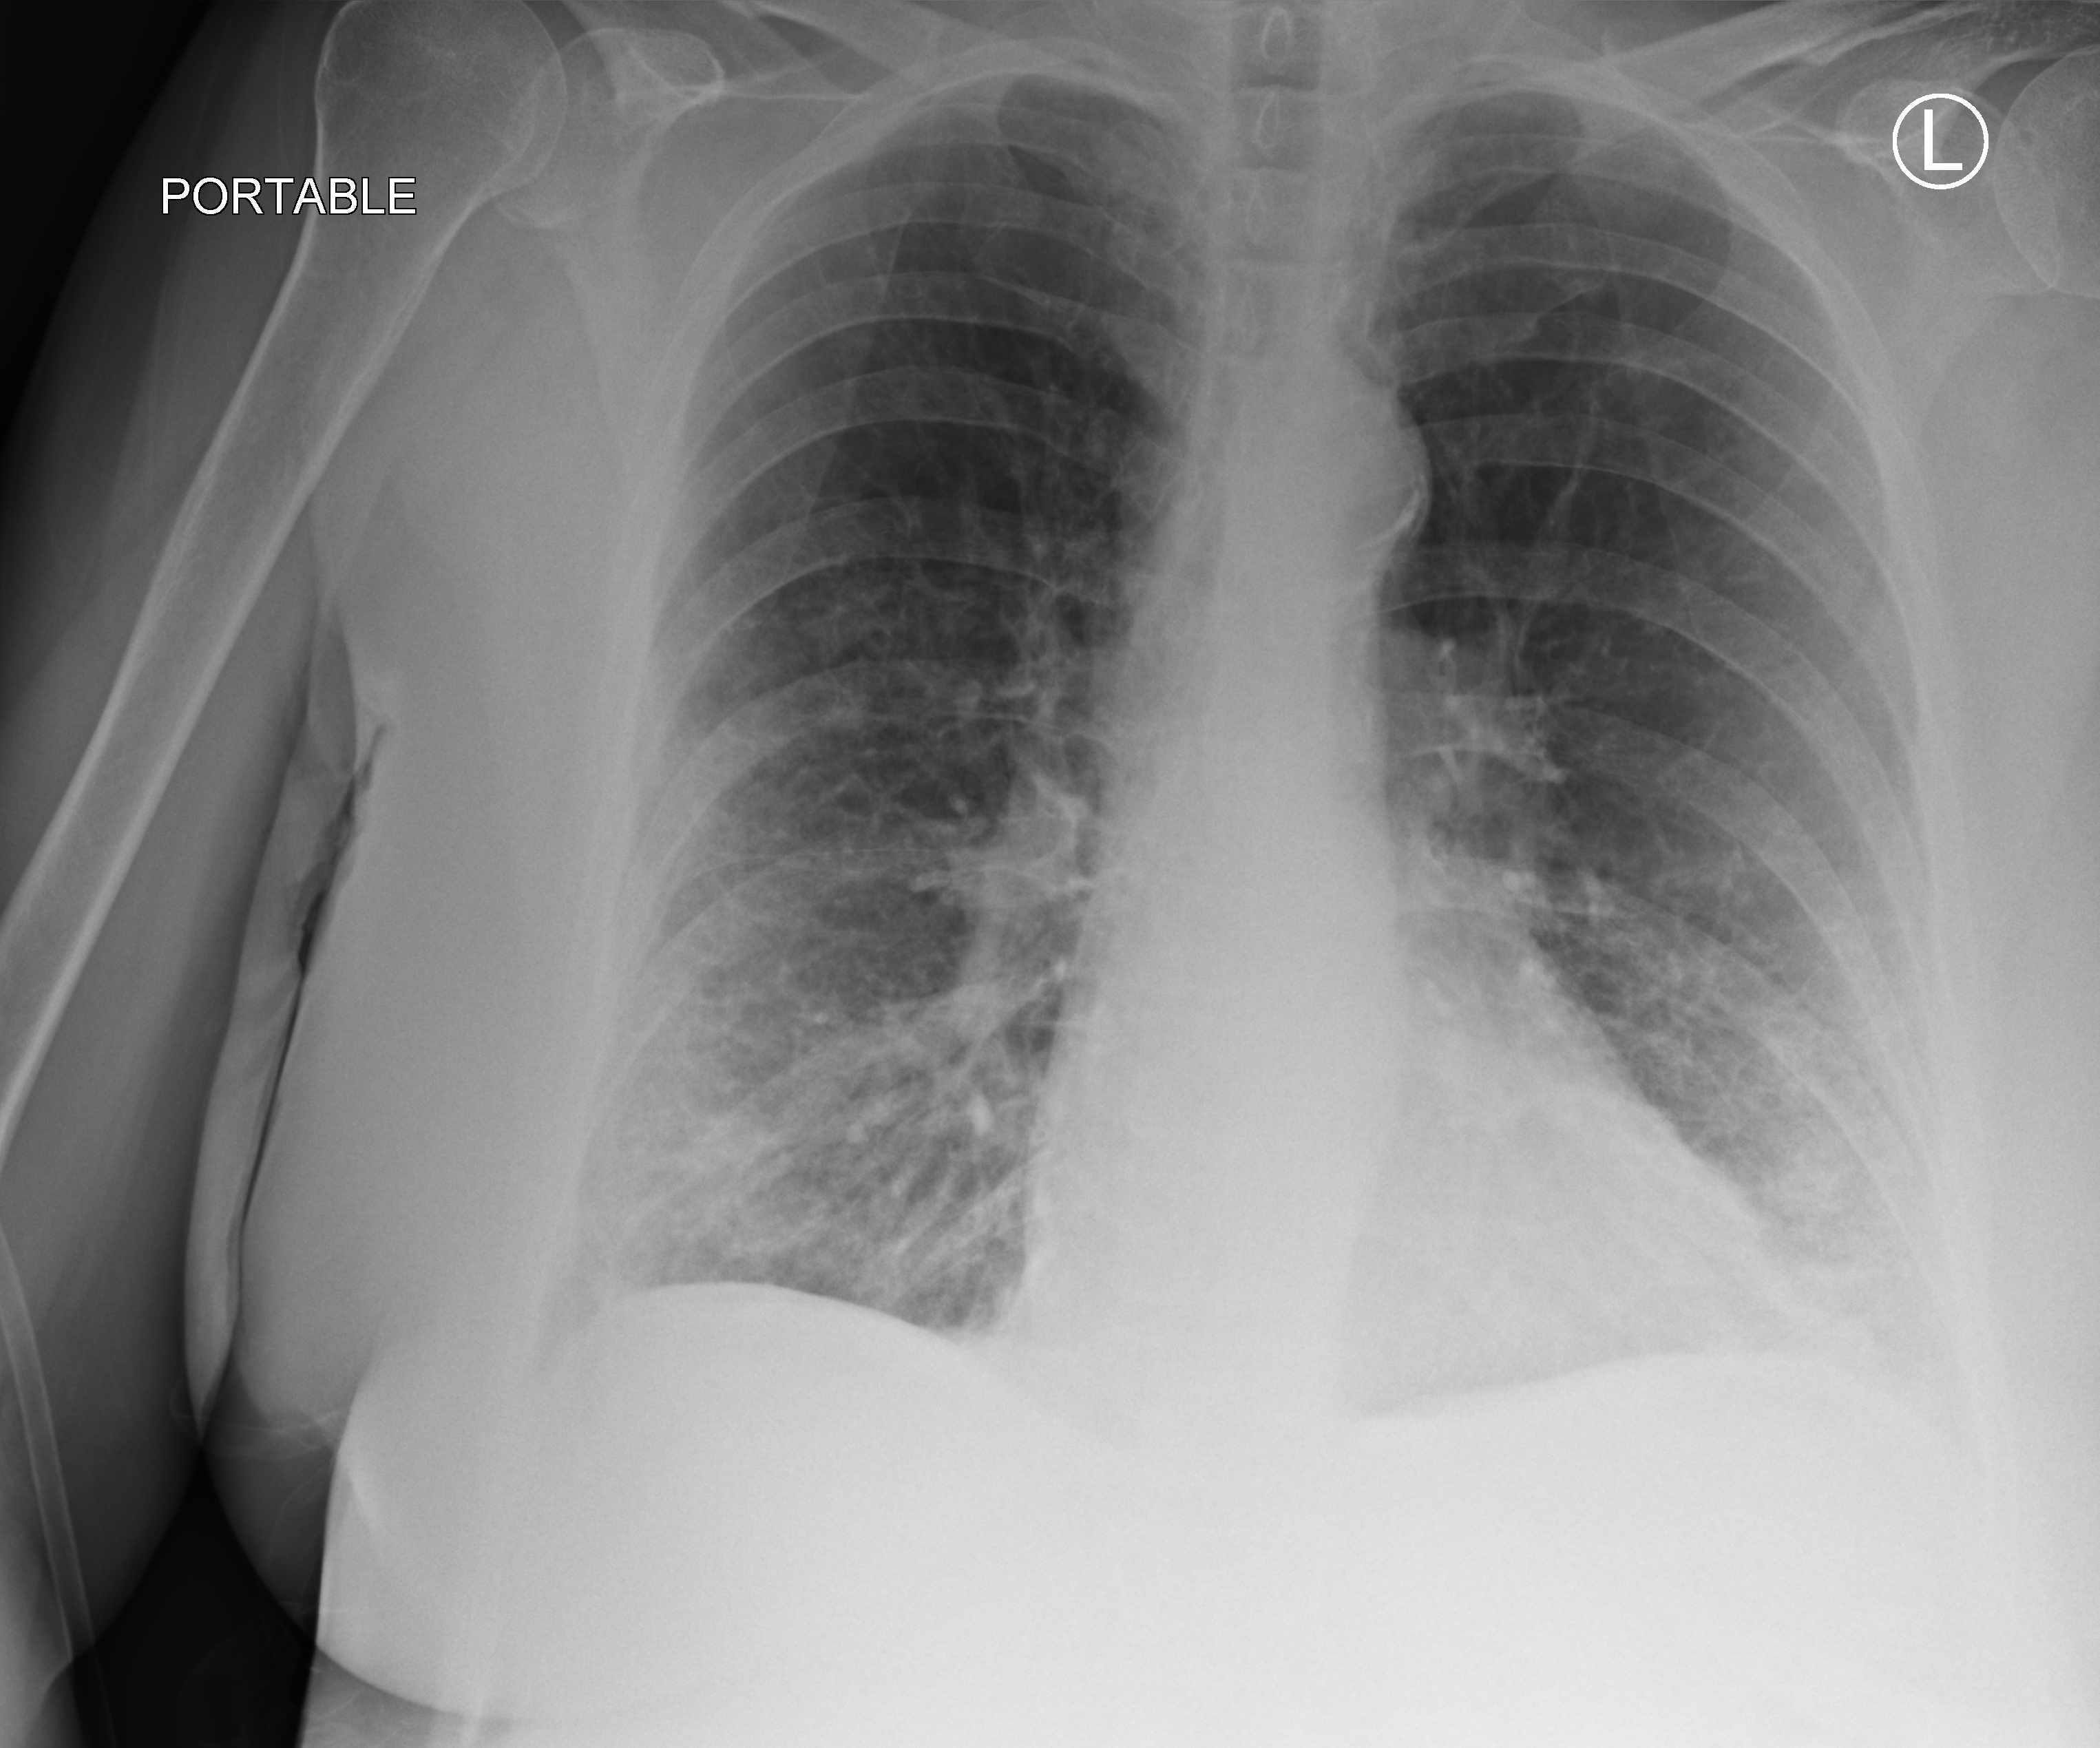
Bedside chest radiograph (computed radiography). Patient hospitalised with COVID-19; female, aged 60–74 years.
Hospital-stay facts (about this admission, not read from this image; timing relative to this image not recorded): mechanically ventilated during this hospital stay: no; other chronic lung disease (admission record): no.